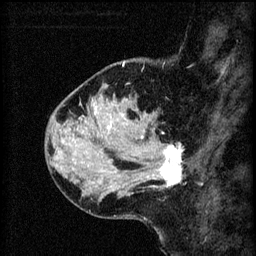
Breast MRI (dynamic contrast-enhanced), one sagittal slice. Slice 20 of 60 in the series (ordered by position). 3 images stored at this slice position (order not interpretable as contrast timing). 1.5 T. TE 4.2 ms, TR 8.2 ms. 256 × 256 image matrix, field of view 180 × 180 mm. Patient: female, 37 years.
Annotated regions visible in this slice (semi-automatic segmentation, software-assisted and operator-edited):
- analysis volume of interest (the breast-tissue region the enhancement analysis was run in; not a lesion): bounding box [x1, y1, x2, y2] px = [124, 138, 190, 195]
- tumour enhancement mask (voxels above the 70 % enhancement threshold inside the analysis volume of interest): [141, 138, 183, 187]